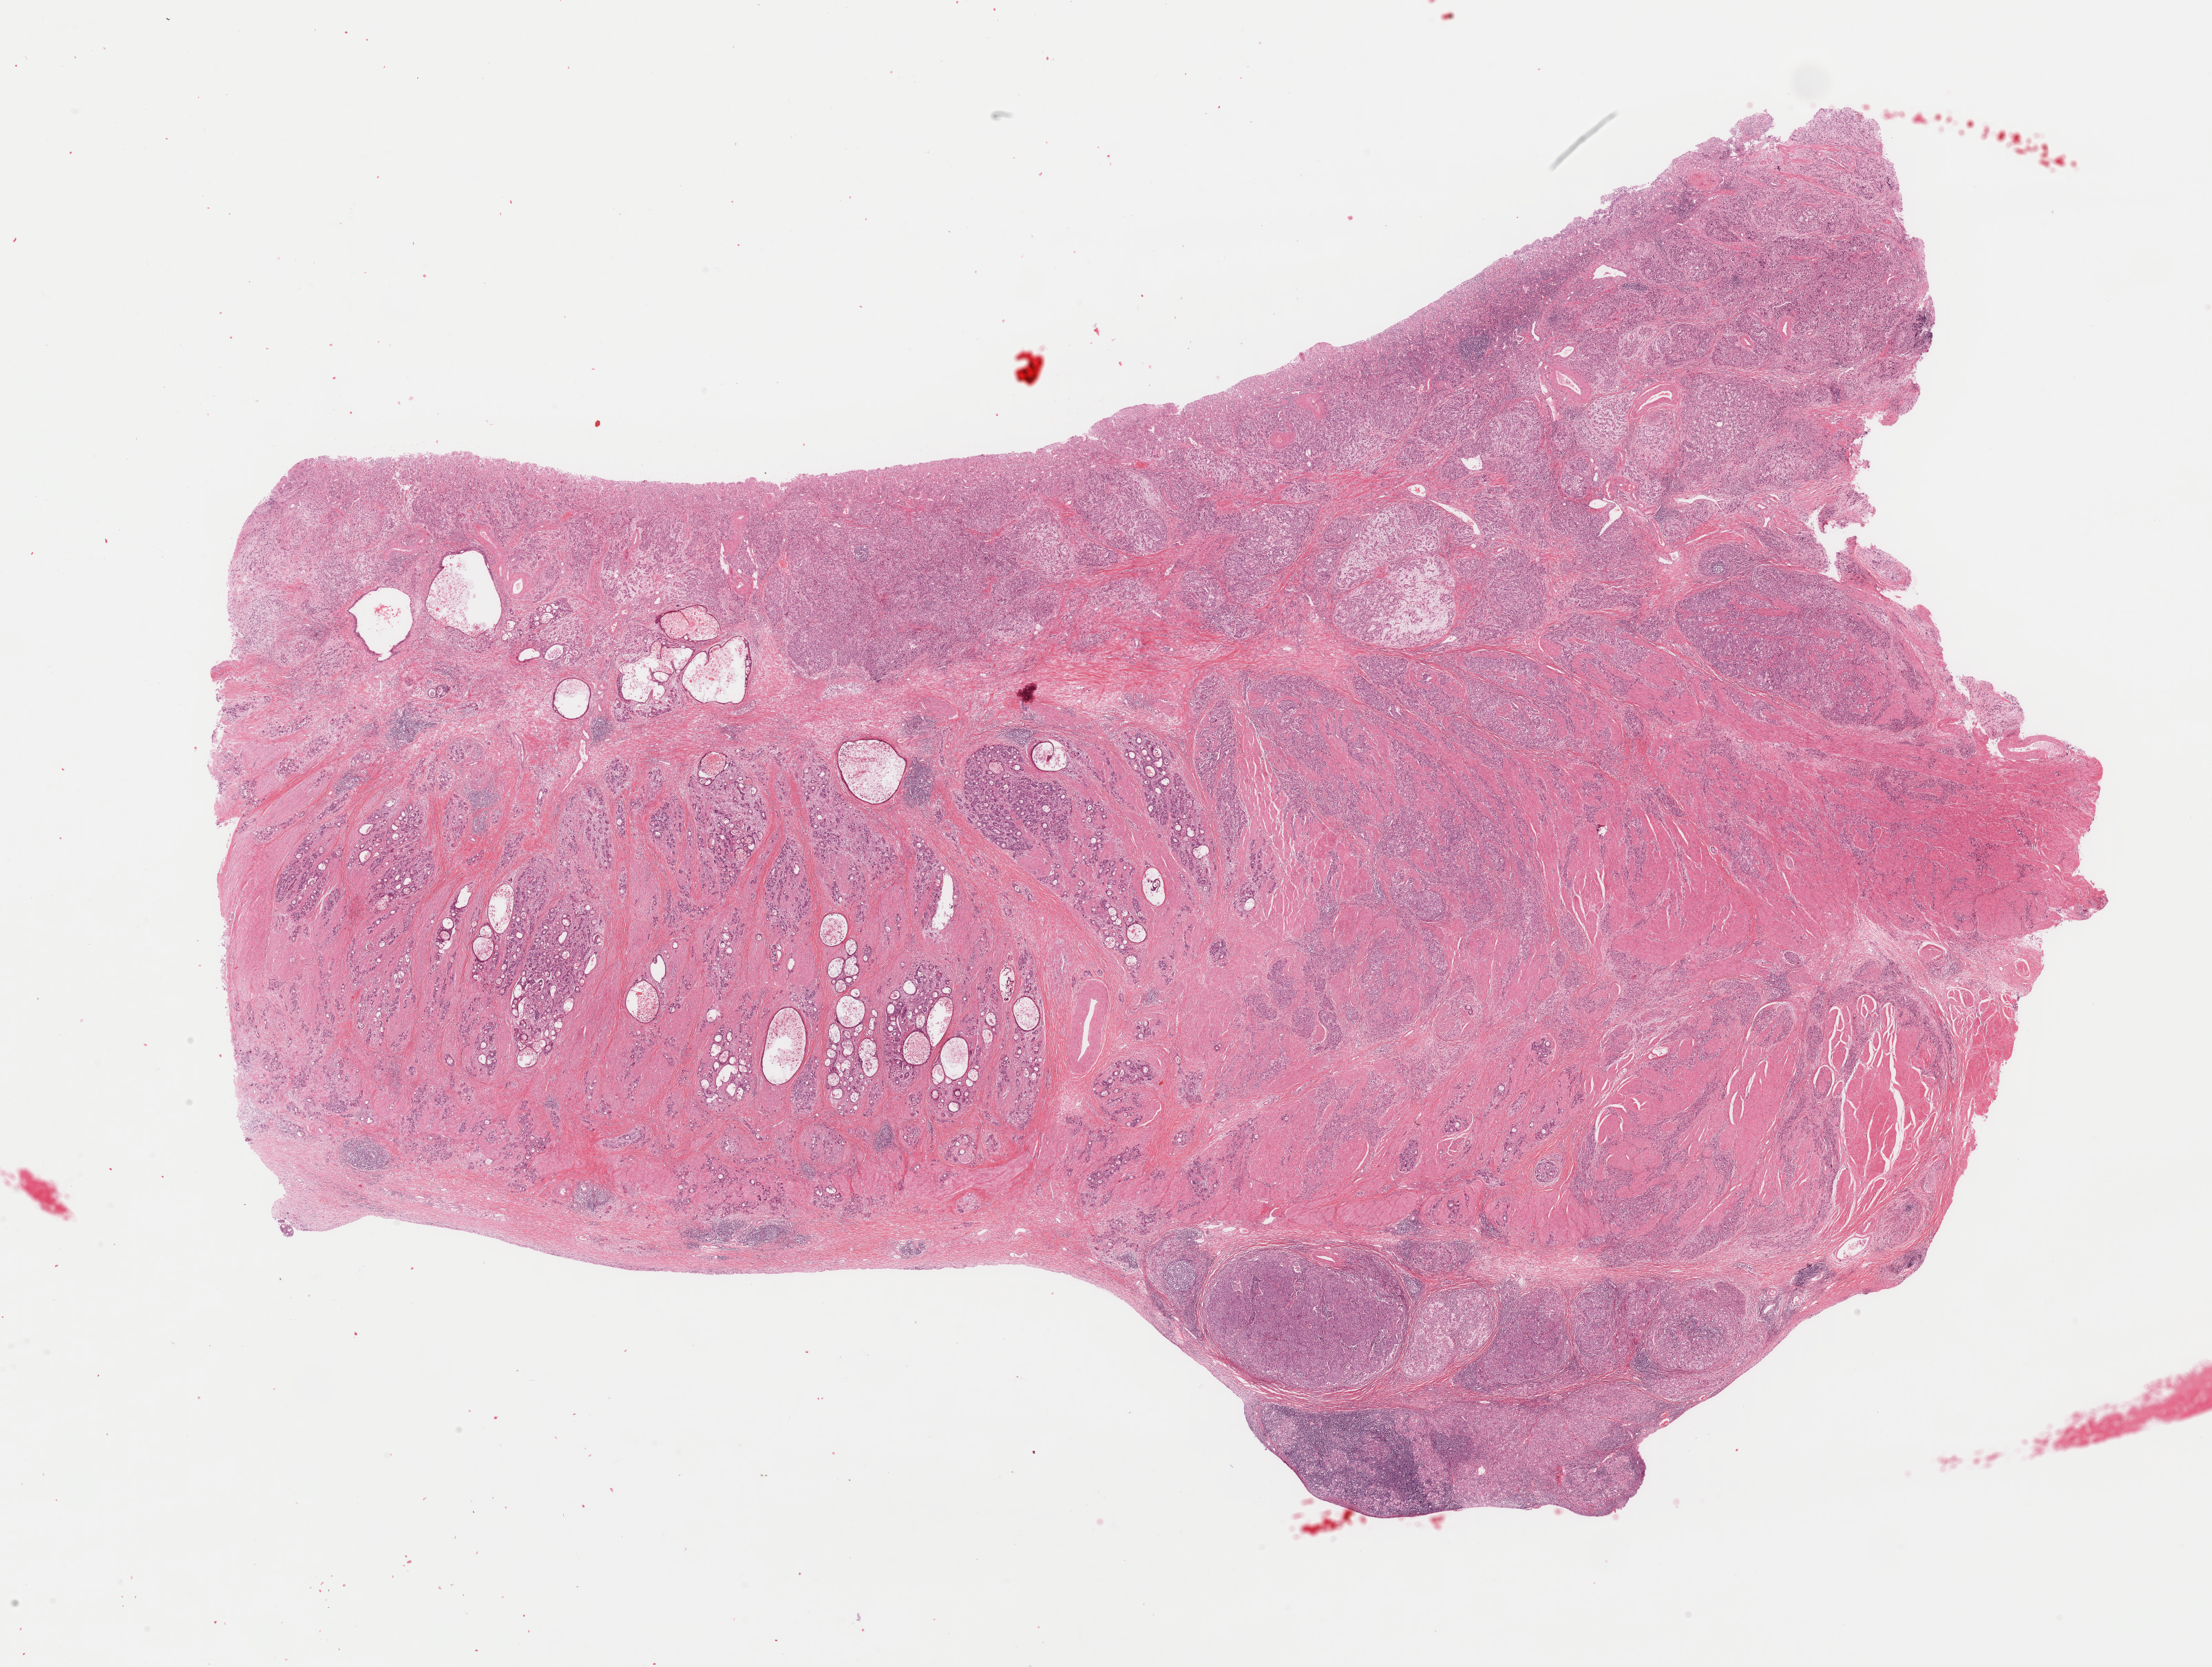
Digitized Hematoxylin and eosin (H&E) stained tissue section (whole slide) — low-resolution overview of the scanned area, about 25.4 x 19.1 mm. Formalin-fixed paraffin-embedded (FFPE) diagnostic section. Primary tumour sample from the stomach. Female patient; age at initial diagnosis 71 years. Histologic grade: G3 (poorly differentiated).
AJCC pathologic stage: IIIB (7th edition). Pathologic diagnosis: Adenocarcinoma, NOS (cardia, NOS).